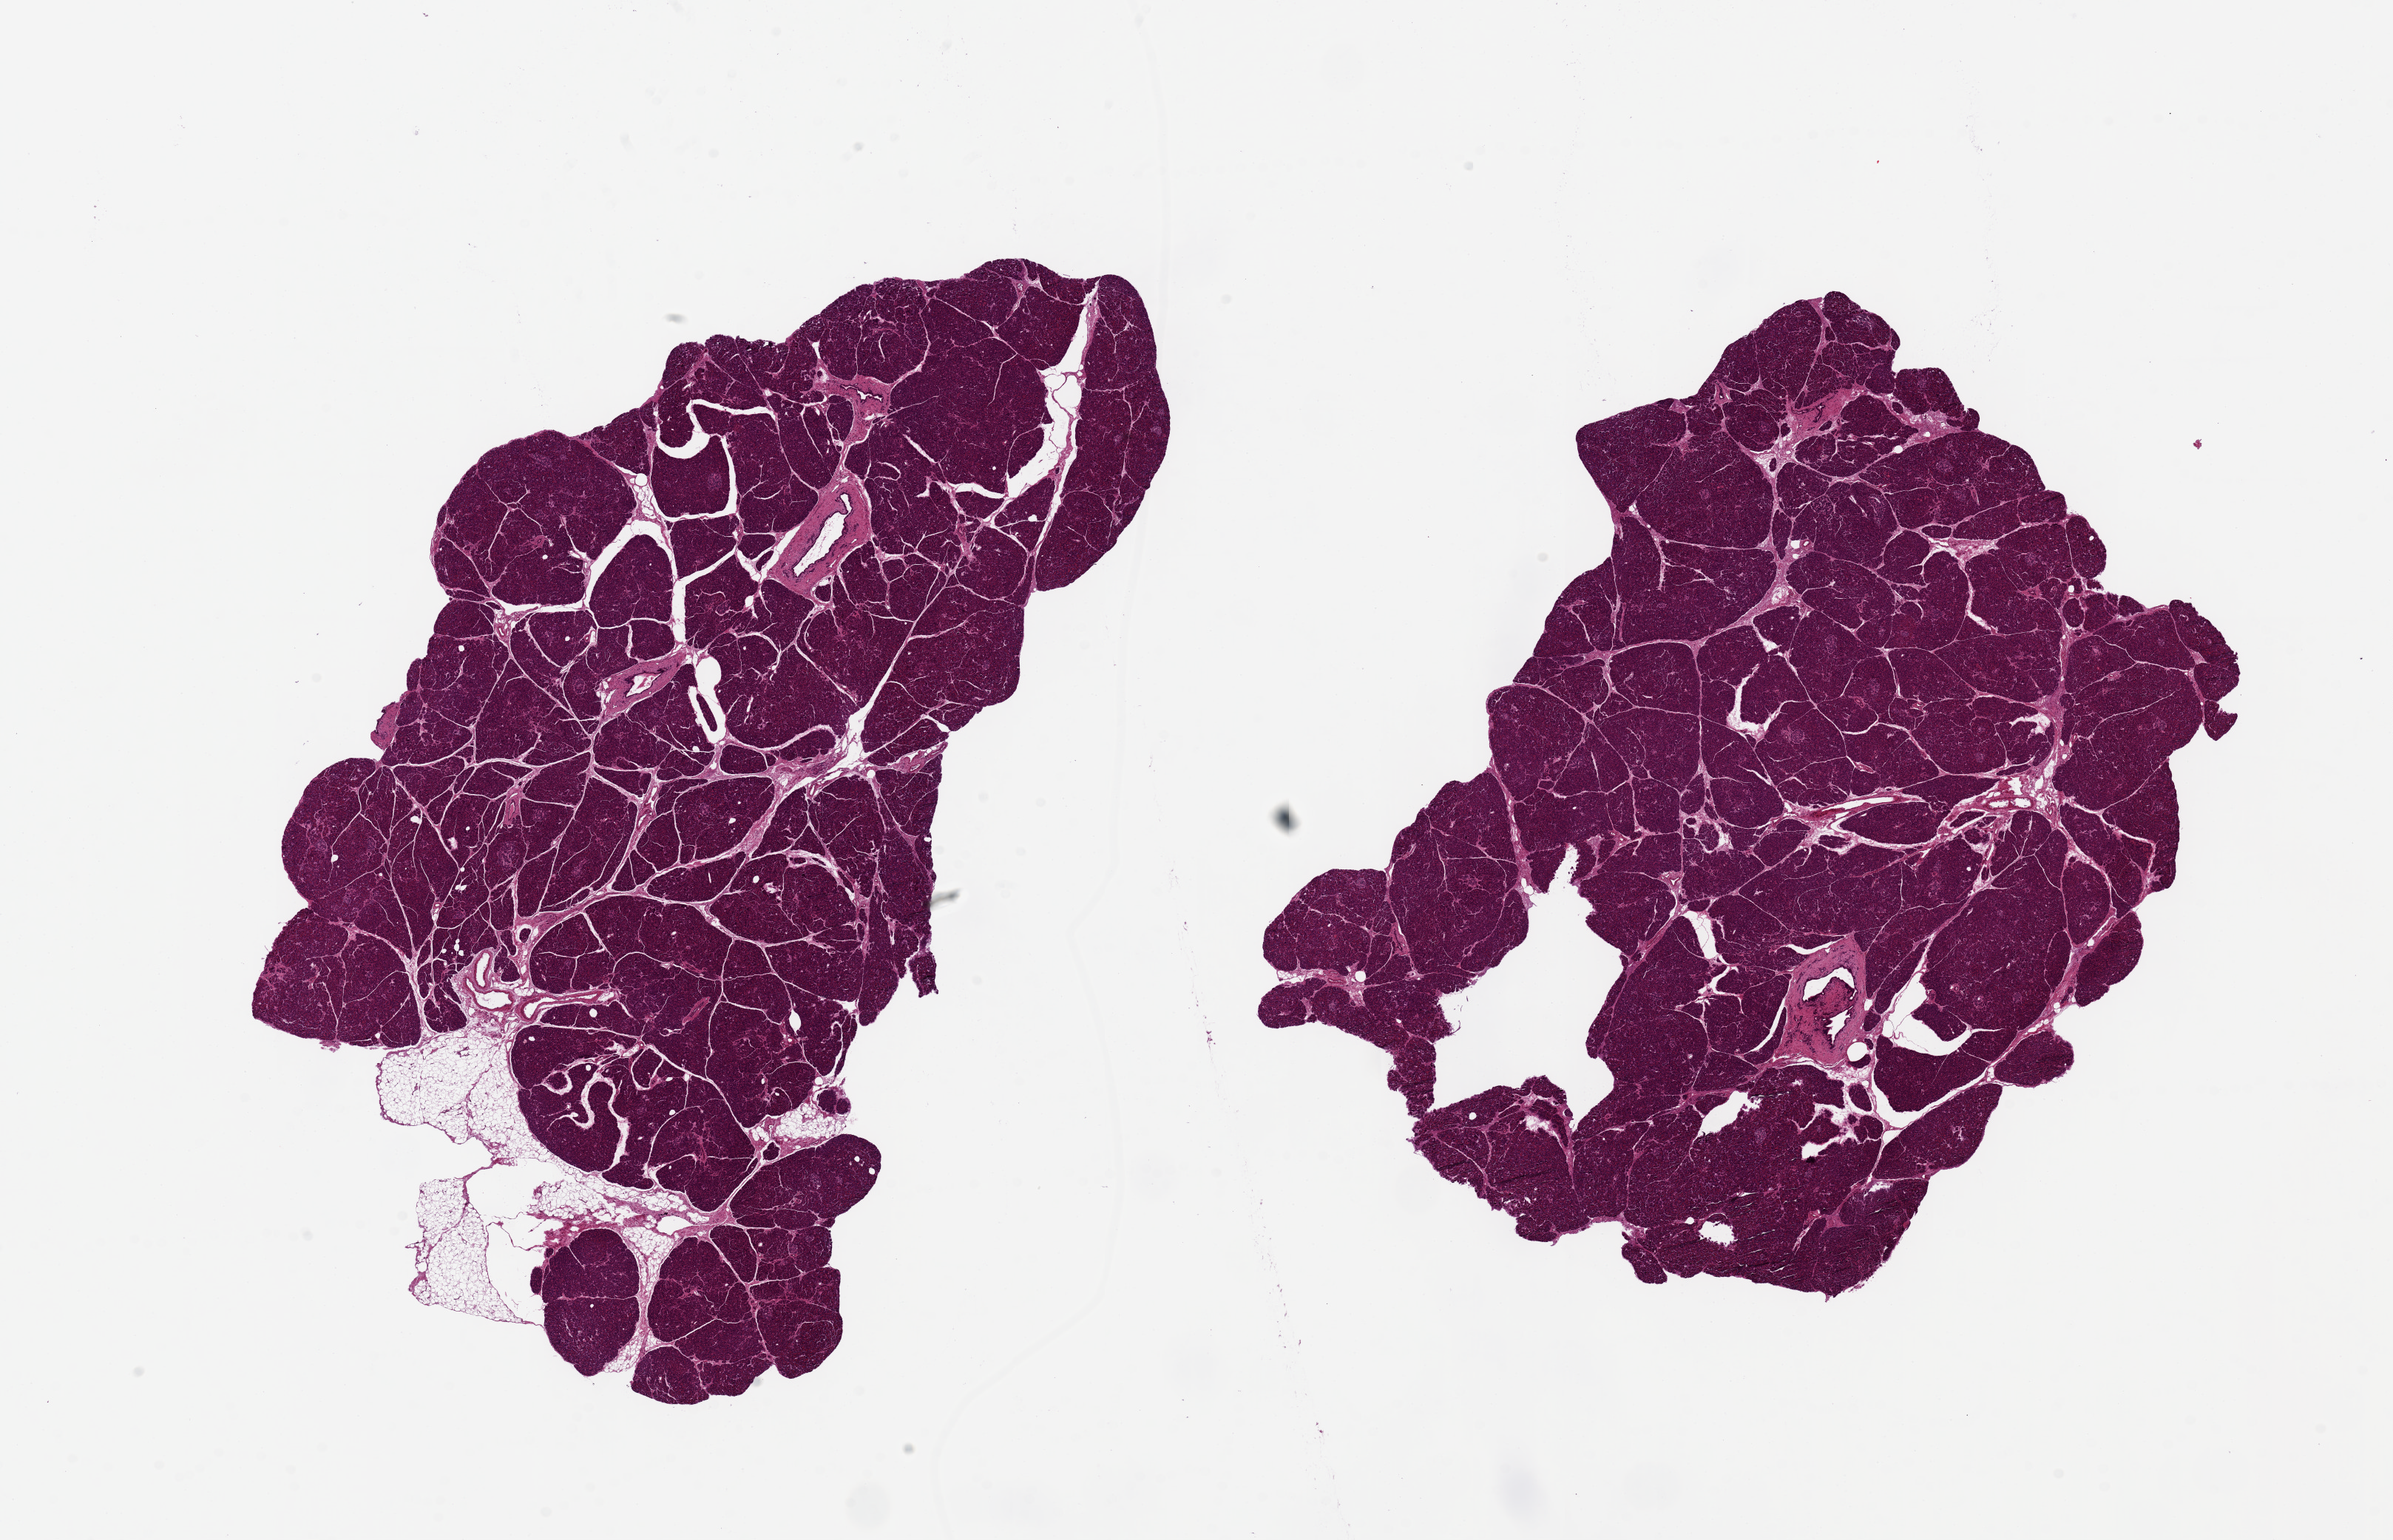
Haematoxylin and eosin whole-slide image — whole scanned area (about 25.6 x 16.5 mm) shown as a low-resolution overview; PAXgene-fixed paraffin-embedded (PFPE) section; section of pancreas (target tissue); tissue donor sample. Donor: female.
* reviewer comment on this tissue sample: 2 pieces, 13x7 & 11x8mm; good morphology; <5% adipose